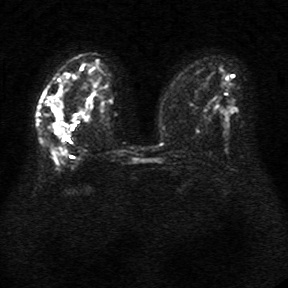
Breast MRI, one axial slice. Position 18 of 34 along the scan axis. Diffusion-weighted series; image 2 of 4 stored at this slice position (different b-values; order by instance number). 1.5 T. 5 mm slice thickness. 288 × 288 image matrix. Female patient.
Structures marked on this image (manually delineated by an expert):
- tumour on diffusion-weighted imaging: bounding box <50,94,66,136> (left, top, right, bottom; pixels)